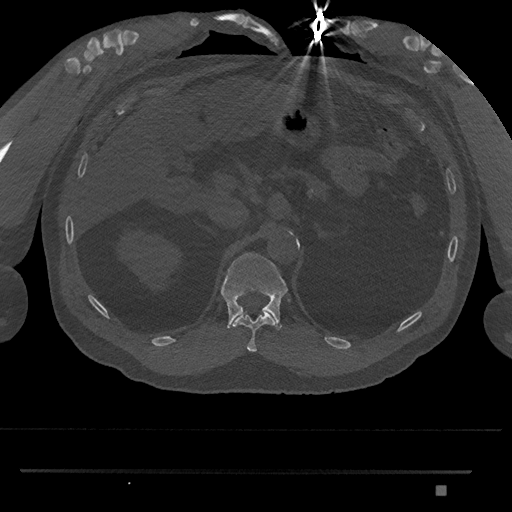
CT including the spine, one axial slice. Position 914 of 1134 along the scan axis. Reconstruction kernel Br40s/3. Bone window (W 1800 / L 400 HU). 0.5 mm slice thickness. 512 × 512 image matrix, field of view 429 × 429 mm. Male patient, age 65 years. From the clinical record (not read from this slice): primary cancer: prostate.
Outlined on this slice (semi-automatically segmented with operator editing):
- T11 vertebra: bounding box (x1, y1, x2, y2) in pixels: (232, 312, 275, 352)
- T12 vertebra: (220, 252, 288, 331)